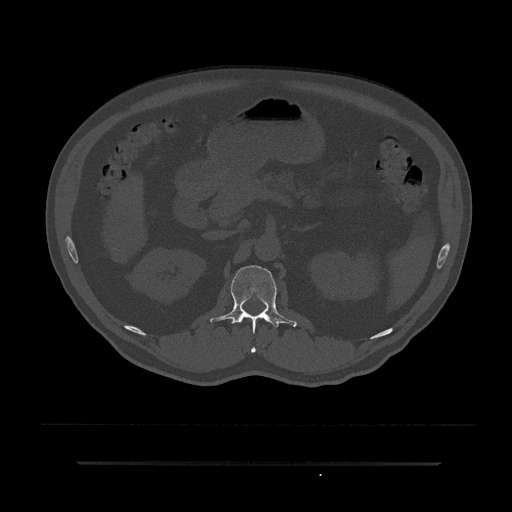
CT including the spine, one axial slice. Position 151 of 797 along the scan axis. Reconstruction kernel Br40s/3. 120 kVp. Bone window (W 1800 / L 400 HU). 512 × 512 image matrix, field of view 464 × 464 mm. Patient: male, 59 years. Case-level facts recorded for this patient, not image findings: primary cancer: bile ducts; vertebrae with lytic lesions (as recorded): T10.
Annotated regions visible in this slice (semi-automatic segmentation, software-assisted and operator-edited):
- L1 vertebra: bounding box (x1, y1, x2, y2) in pixels: (210, 265, 297, 353)